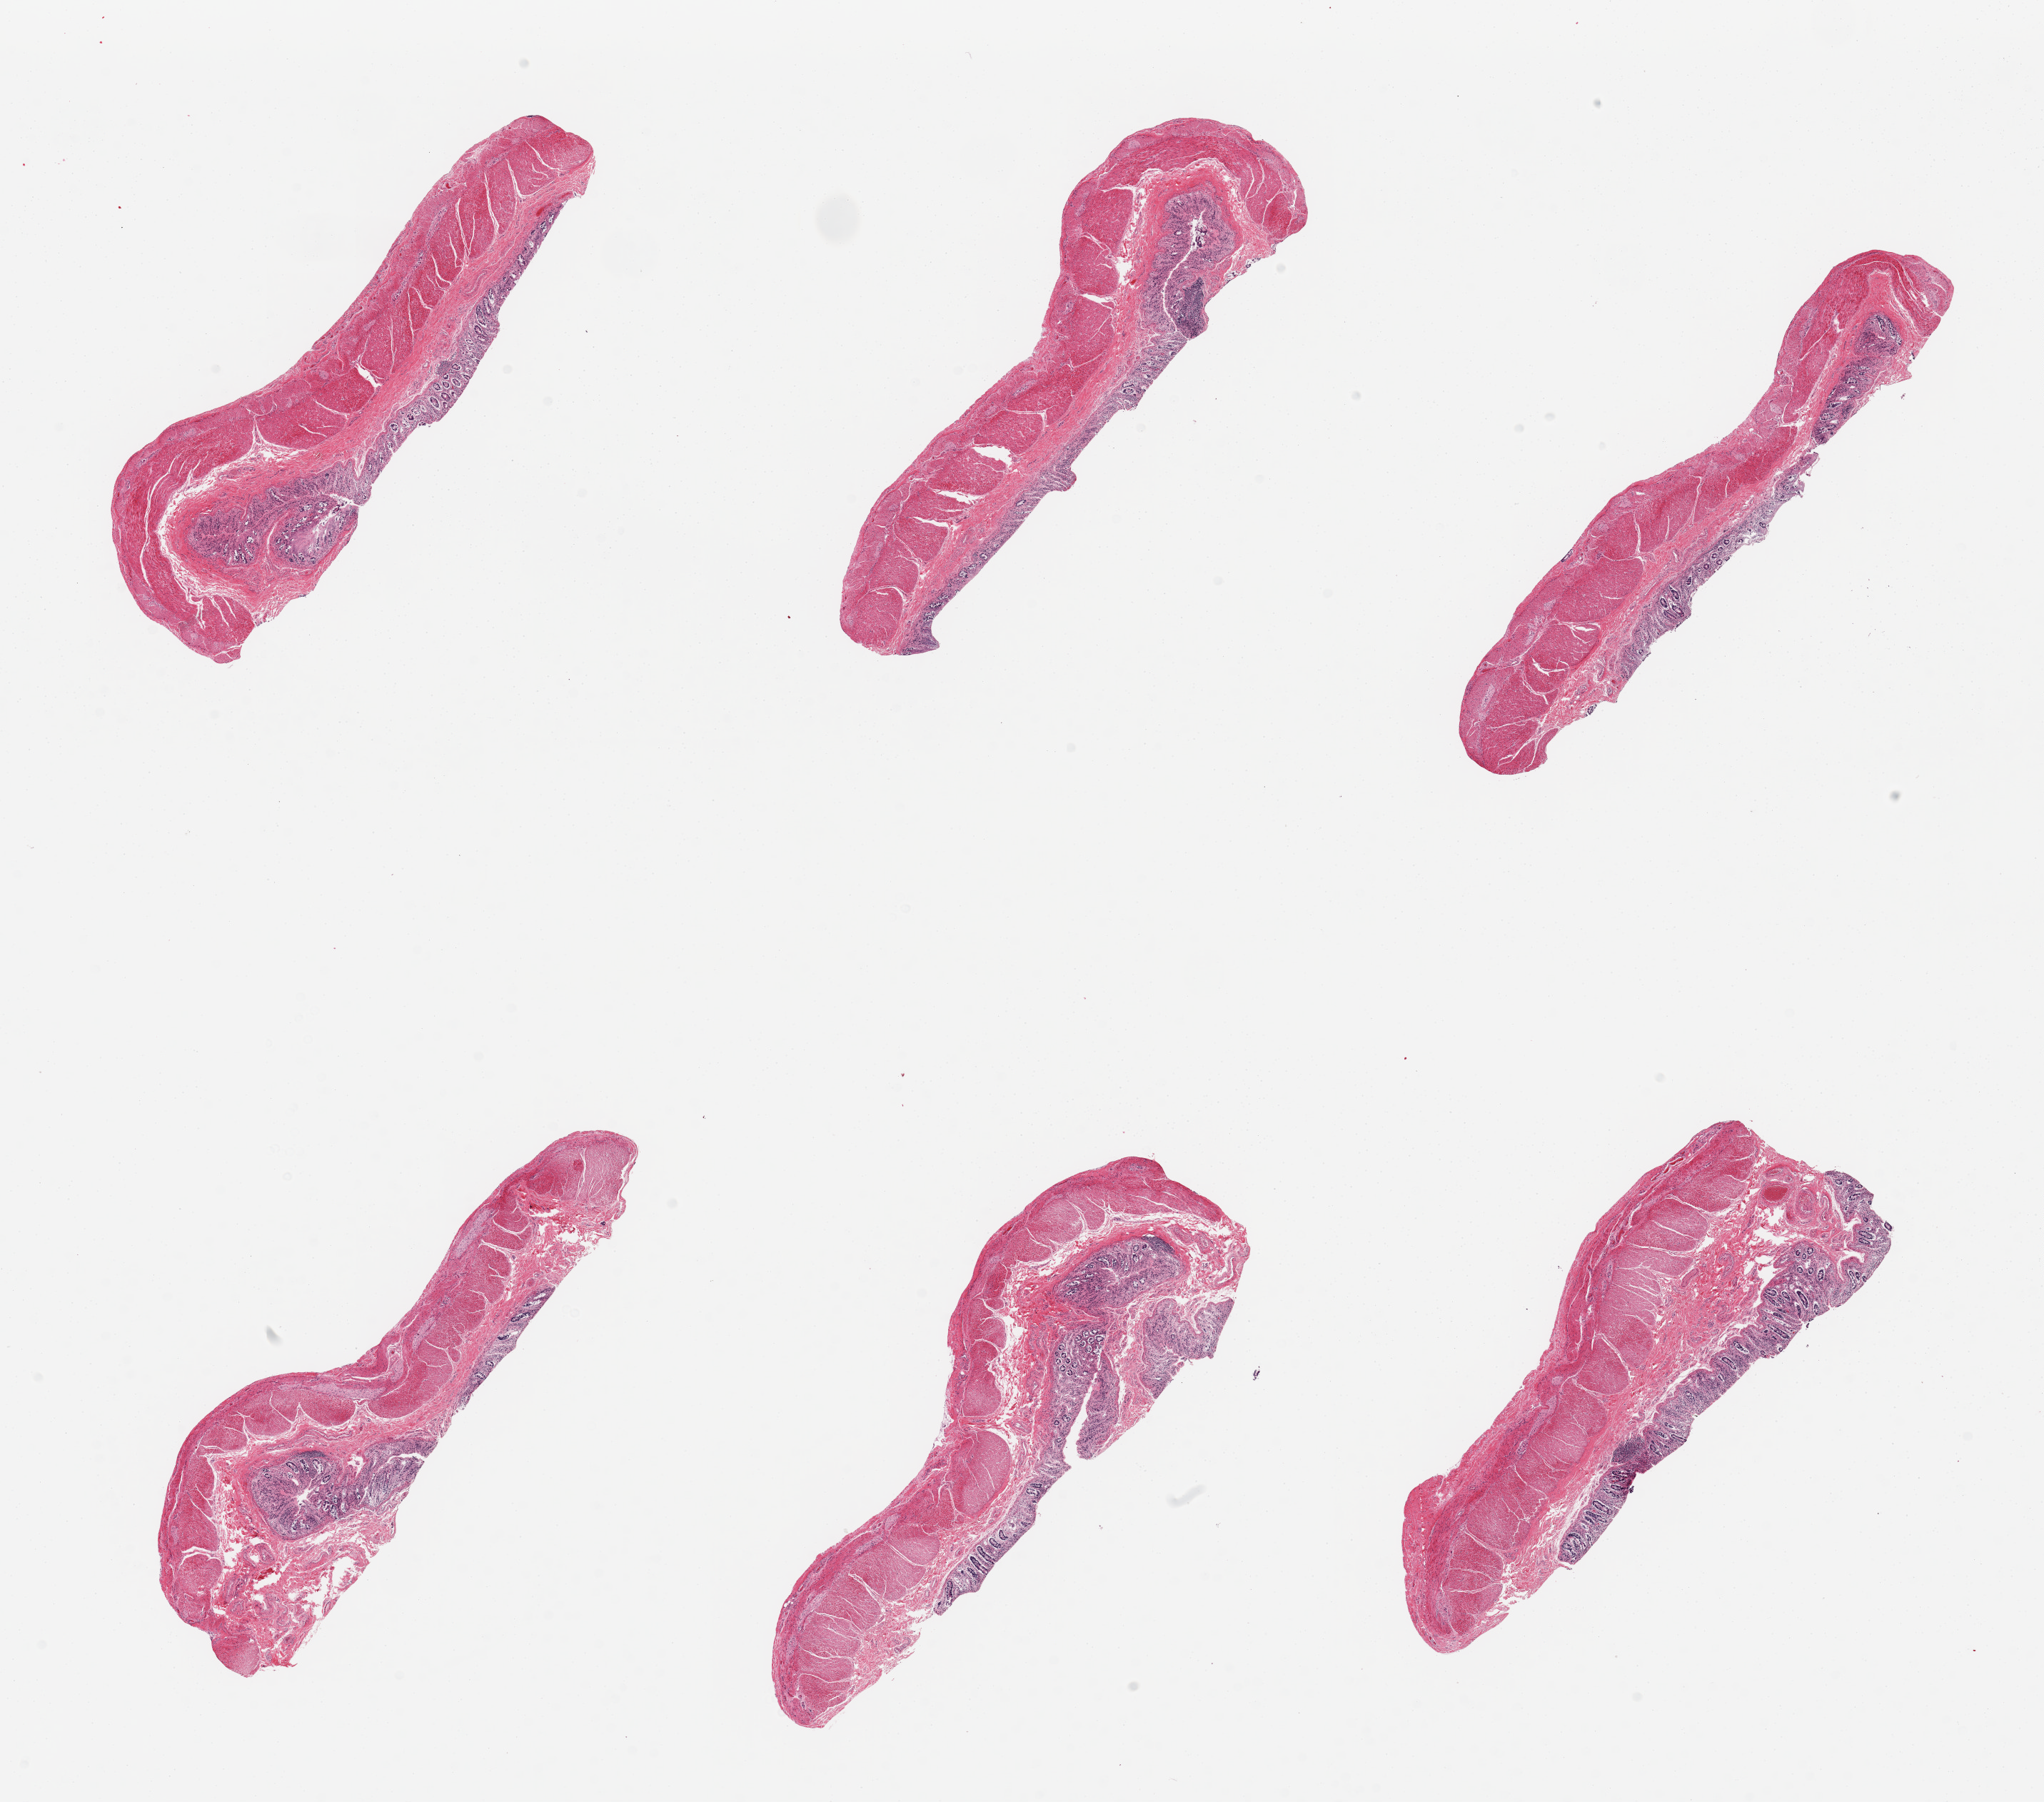
Digitized haematoxylin and eosin-stained section, shown as a low-resolution overview of the whole scanned area (about 22.6 x 20.0 mm); PAXgene-fixed paraffin-embedded (PFPE) section; target tissue: transverse colon; donor tissue sample. Male donor.
Pathologist's review note for this sample: 6 pieces: all full thickness. well trimmed; mucosa largely severely autolyzed; muscle slightly autolyzed.